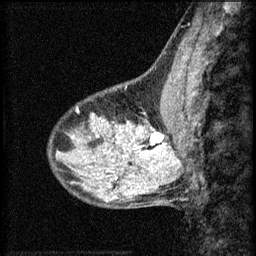
Breast MRI (dynamic contrast-enhanced), one sagittal slice. Slice 19 of 60 in the series (ordered by position). 3 images stored at this slice position (order not interpretable as contrast timing). 1.5 T. TE 4.2 ms, TR 8.2 ms. 2 mm slice thickness. 256 × 256 image matrix, field of view 180 × 180 mm. Patient: female, 40 years.
Outlined on this slice (semi-automatic segmentation, software-assisted and operator-edited):
- analysis volume of interest (the breast-tissue region the enhancement analysis was run in; not a lesion): bounding box (x1, y1, x2, y2) in pixels: (108, 108, 167, 159)
- tumour enhancement mask (voxels above the 70 % enhancement threshold inside the analysis volume of interest): (138, 128, 165, 155)